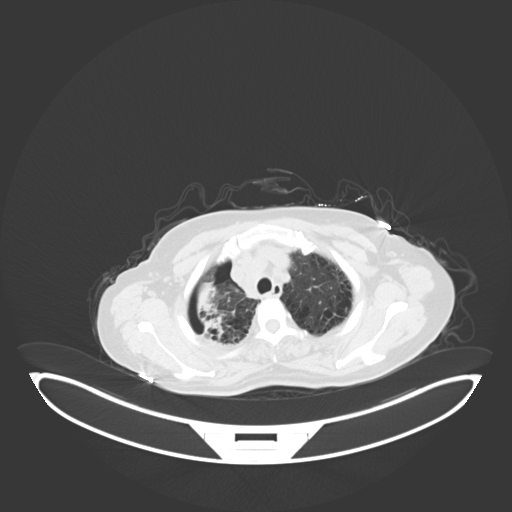
Chest CT, one axial slice. Slice 53 of 69 in the series (ordered by position). Lung window (W 1500 / L -600 HU). 512 × 512 image matrix. Female patient, age 64 years. From the clinical record (not read from this slice): clinical TNM (as recorded): T3 N3 M0.
Structures marked on this image (bounding box drawn by a radiologist):
- lung tumour (recorded histology: squamous cell carcinoma): box from (x=189, y=274) to (x=227, y=339) px